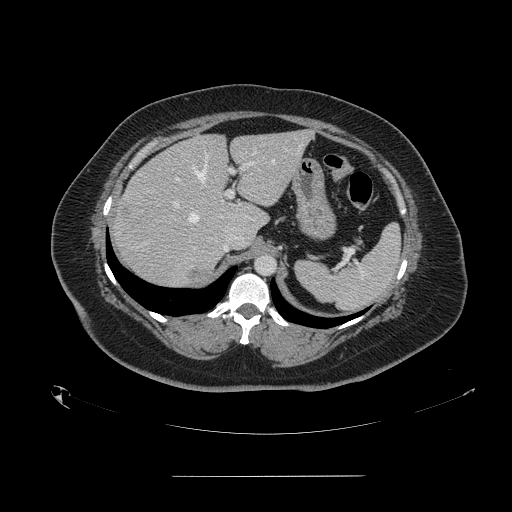
Contrast-enhanced abdominal CT, one axial slice; slice 107 of 164 in the series (ordered by position); 120 kVp; intravenous contrast given; soft-tissue window (W 400 / L 40 HU); 2.5 mm slice thickness; 512 × 512 image matrix, field of view 495 × 495 mm. Female patient, age 52 years. Case-level facts recorded for this patient, not image findings: diagnosis: colorectal cancer liver metastases, imaged before liver resection; multiple liver metastases: yes; largest metastasis: 3.5 cm; disease in both lobes: no.
Structures marked on this image (outlined manually by an expert reader):
- hepatic veins: bounding box <188,147,300,222> (left, top, right, bottom; pixels)
- liver: <113,131,309,288>
- planned liver remnant (the part of the liver to remain after resection): <173,131,310,231>
- portal vein (with intrahepatic branches): <173,162,254,207>
- liver metastasis: <189,270,212,277>
- liver metastasis: <250,211,260,222>
- liver metastasis: <124,208,131,216>